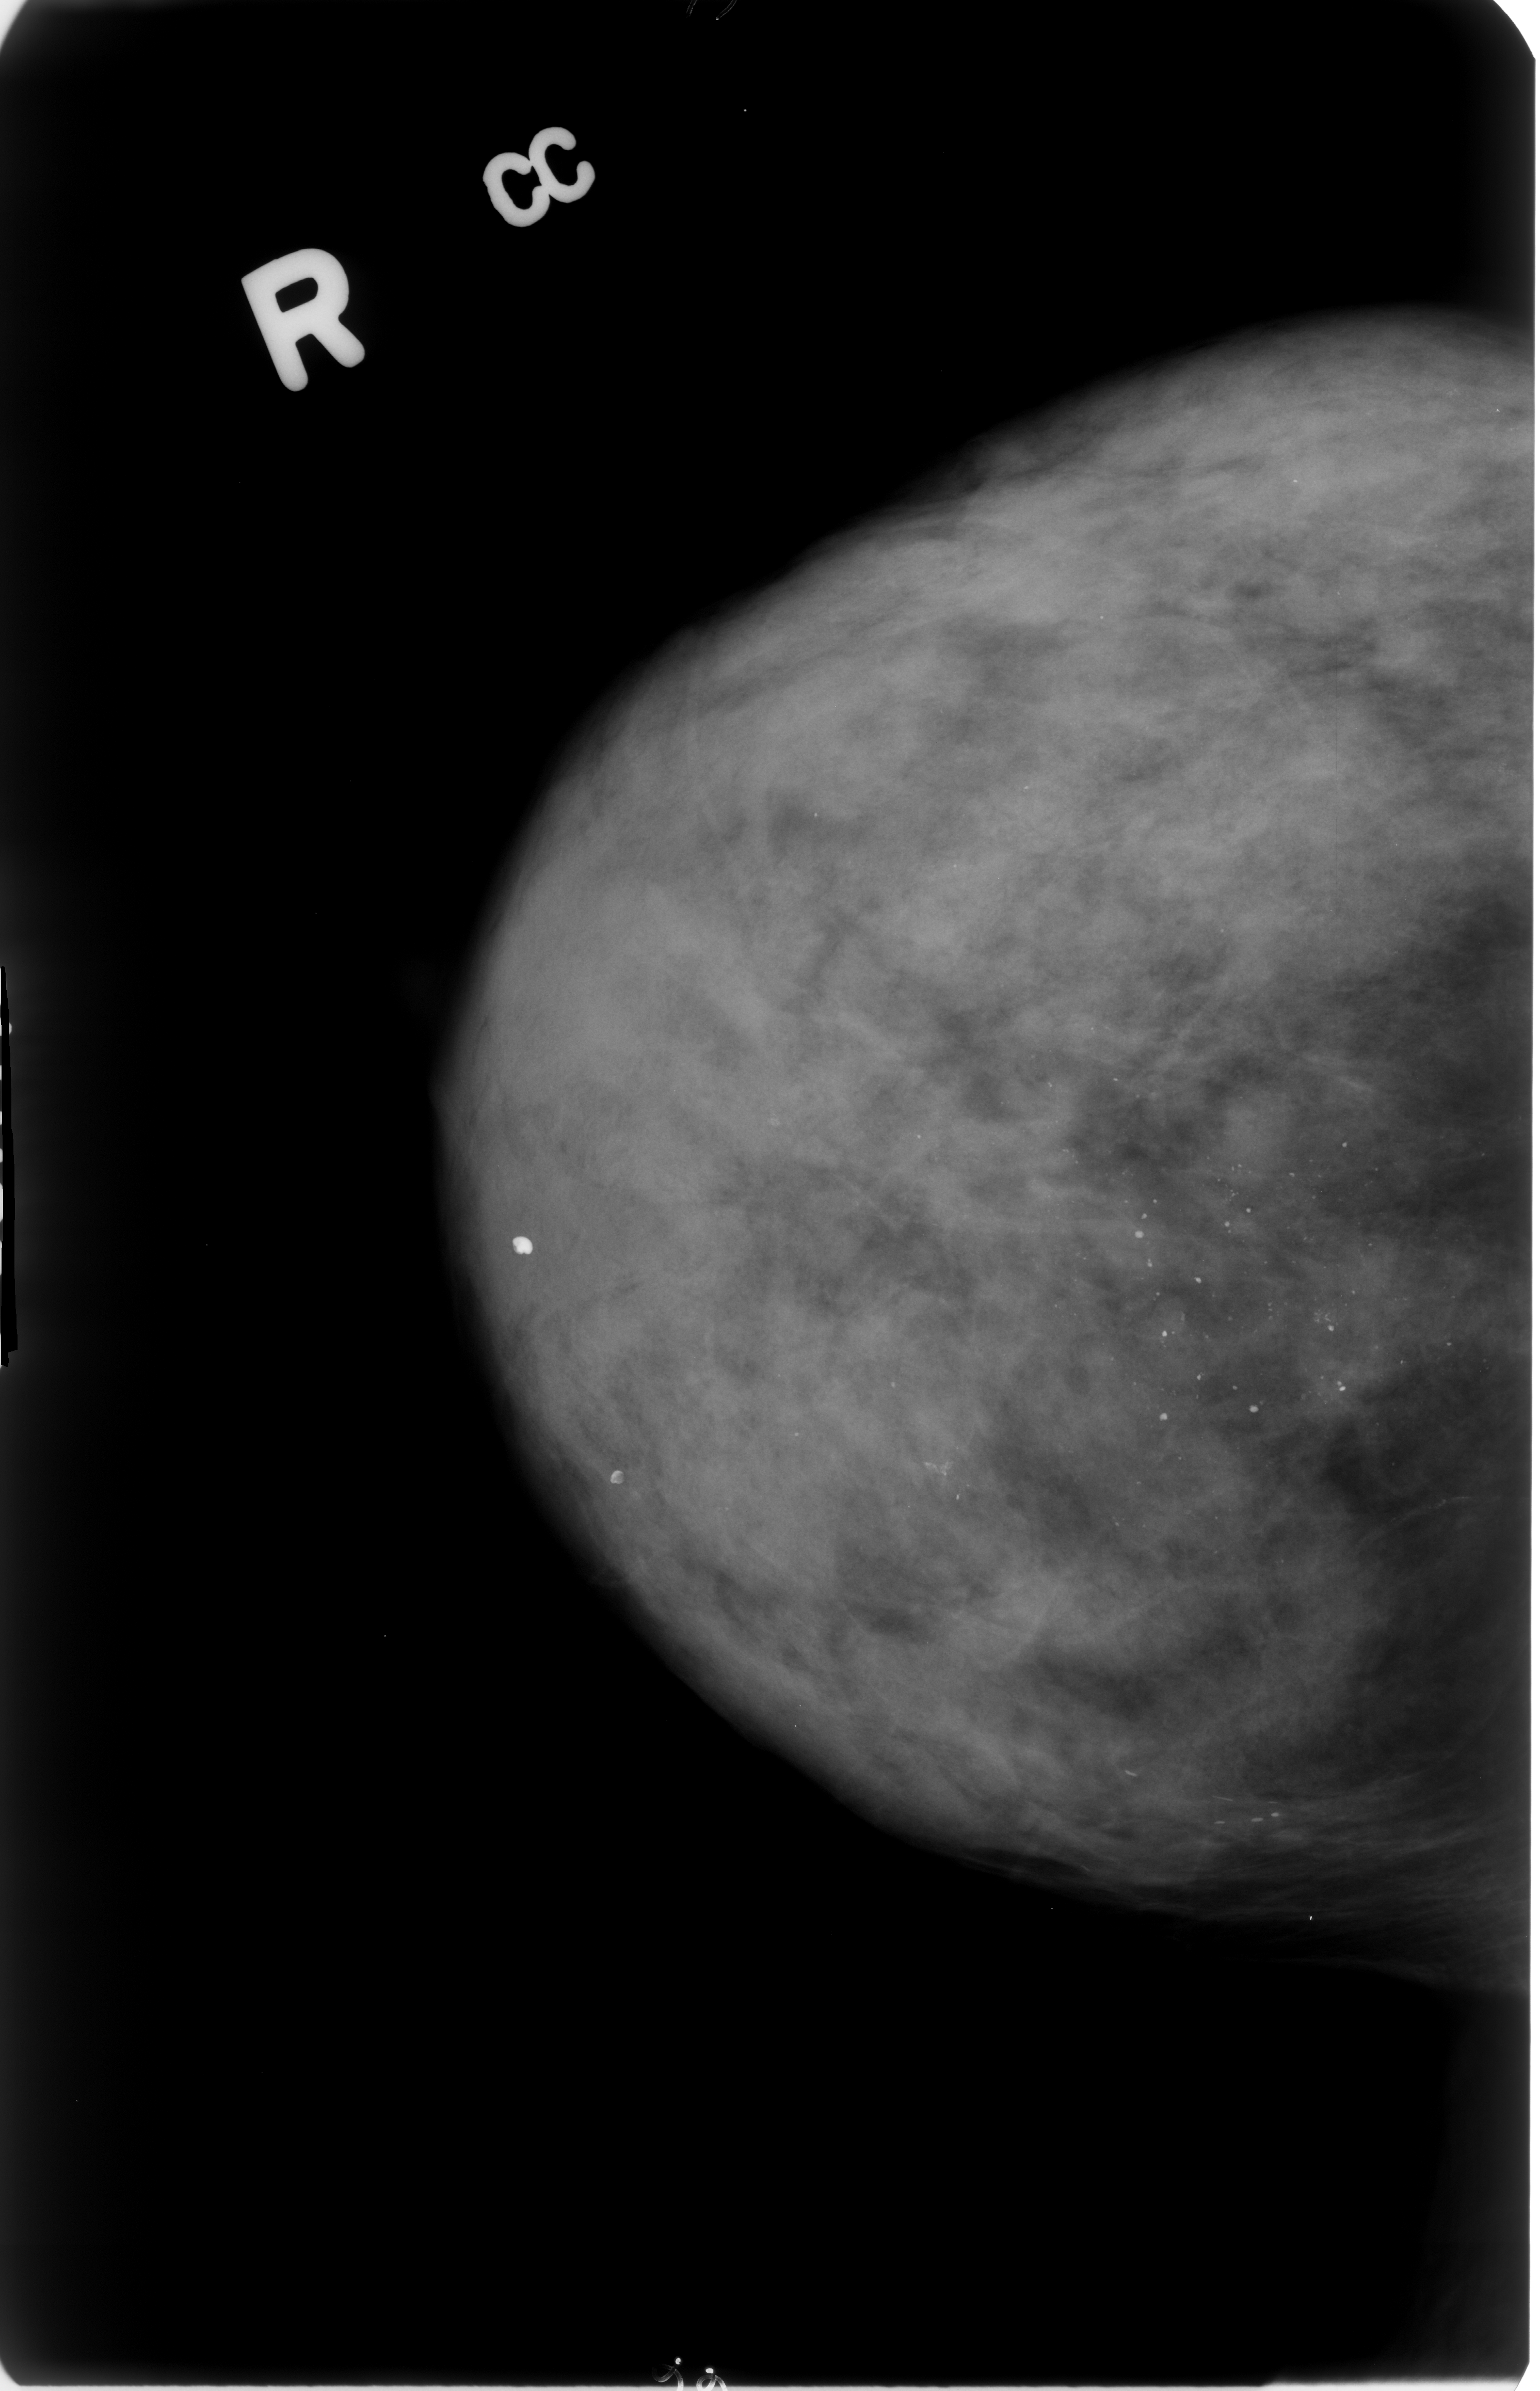
Digitized screen-film mammogram; right breast; CC view; breast composition: extremely dense (BI-RADS density category 4 of 4).
Marked findings (only marked abnormalities are described; nothing is implied about the rest of the image): calcifications, morphology vascular / coarse / lucent center / round and regular / punctate, distribution regional; BI-RADS assessment category 2; subtlety rating 5 on a 1 (subtle) to 5 (obvious) scale; benign without callback (not worked up further).